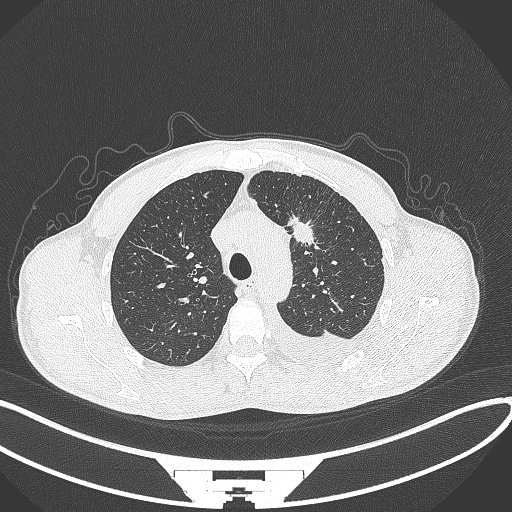
Chest CT, one axial slice; slice 249 of 371 in the series (ordered by position); reconstruction kernel B70f; 120 kVp; lung window (W 1500 / L -600 HU); 512 × 512 image matrix, field of view 400 × 400 mm. Patient: male, 49 years. From the clinical record (not read from this slice): clinical TNM (as recorded): T1c N1 M1.
Outlined on this slice (rectangle marked by the reading radiologist):
- lung tumour (recorded histology: adenocarcinoma): bounding box [x1, y1, x2, y2] px = [286, 215, 317, 252]